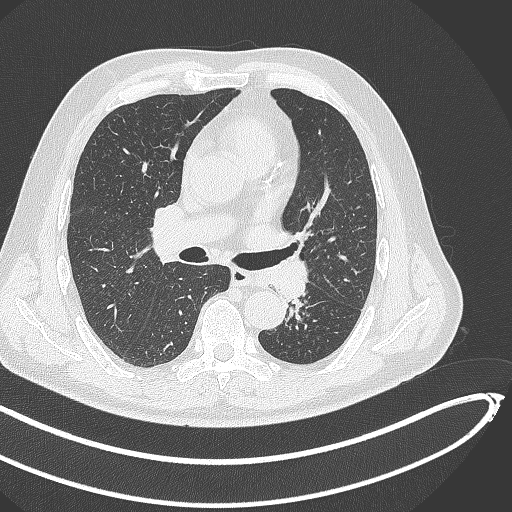
Chest CT, one axial slice. Position 268 of 468 along the scan axis. Reconstruction kernel B70f. 120 kVp. Lung window (W 1500 / L -600 HU). 1 mm slice thickness. 512 × 512 image matrix, field of view 400 × 400 mm. Patient: male, 64 years. Case-level facts recorded for this patient, not image findings: clinical TNM (as recorded): T1c N0 M0; histopathological grade: G2.
Annotated regions visible in this slice (rectangle marked by the reading radiologist):
- lung tumour (recorded histology: squamous cell carcinoma): bounding box <257,261,315,310> (left, top, right, bottom; pixels)